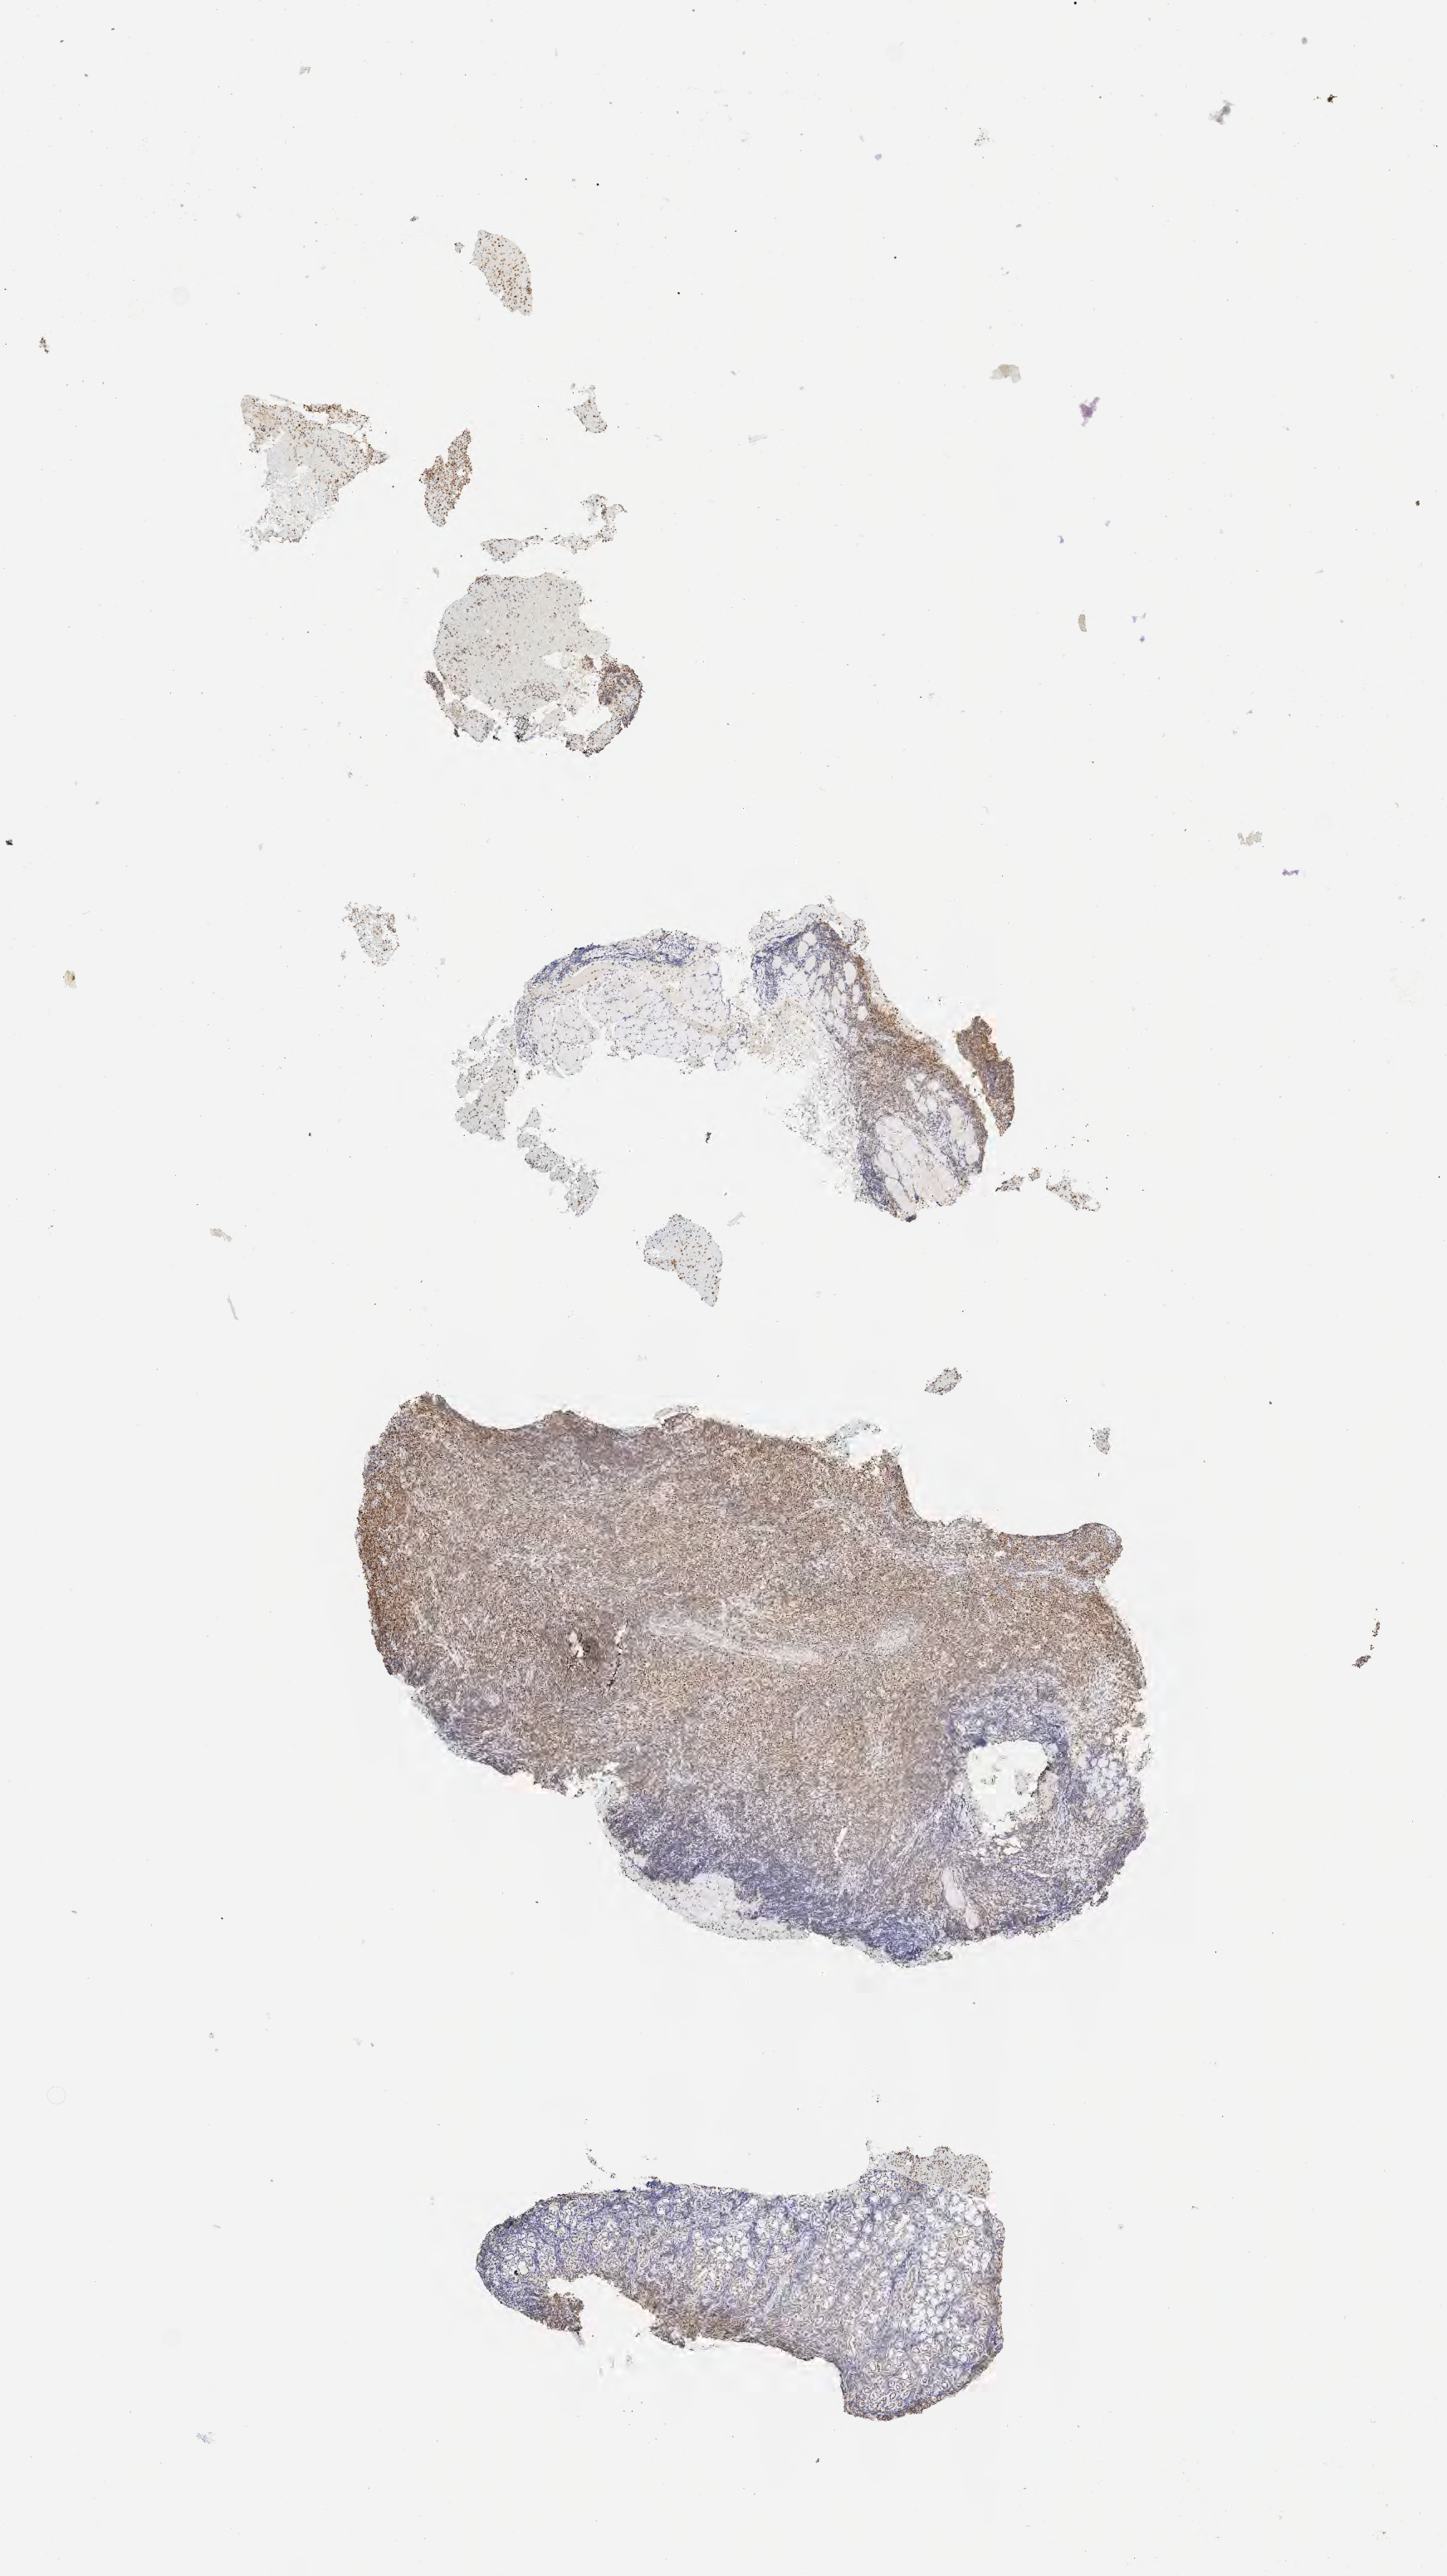
Immunohistochemistry (IHC) whole-slide image stained for BCL6, shown as a low-resolution overview of the whole scanned area (about 7.0 x 12.5 mm). Tumor tissue. Patient: male, age 53 years.
* histologic diagnosis: Diffuse large B-cell lymphoma, NOS